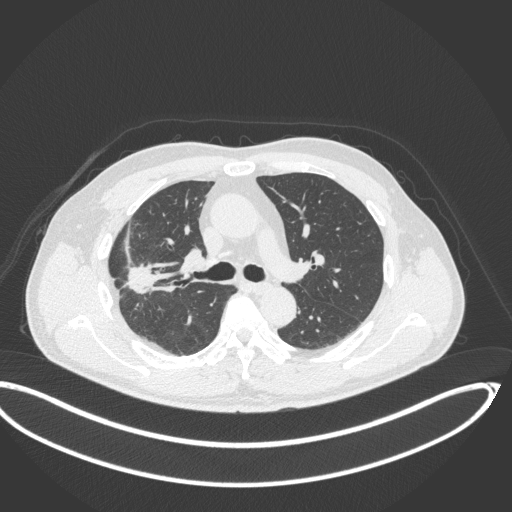
Chest CT, one axial slice. Position 219 of 341 along the scan axis. Reconstruction kernel B31f. 120 kVp. Lung window (W 1500 / L -600 HU). 1 mm slice thickness. 512 × 512 image matrix, field of view 439 × 439 mm. Male patient, age 63 years. From the clinical record (not read from this slice): clinical TNM (as recorded): T1c N0 M0; histopathological grade: G2-3.
Structures marked on this image (bounding box drawn by a radiologist):
- lung tumour (recorded histology: adenocarcinoma): bounding box <123,257,157,299> (left, top, right, bottom; pixels)